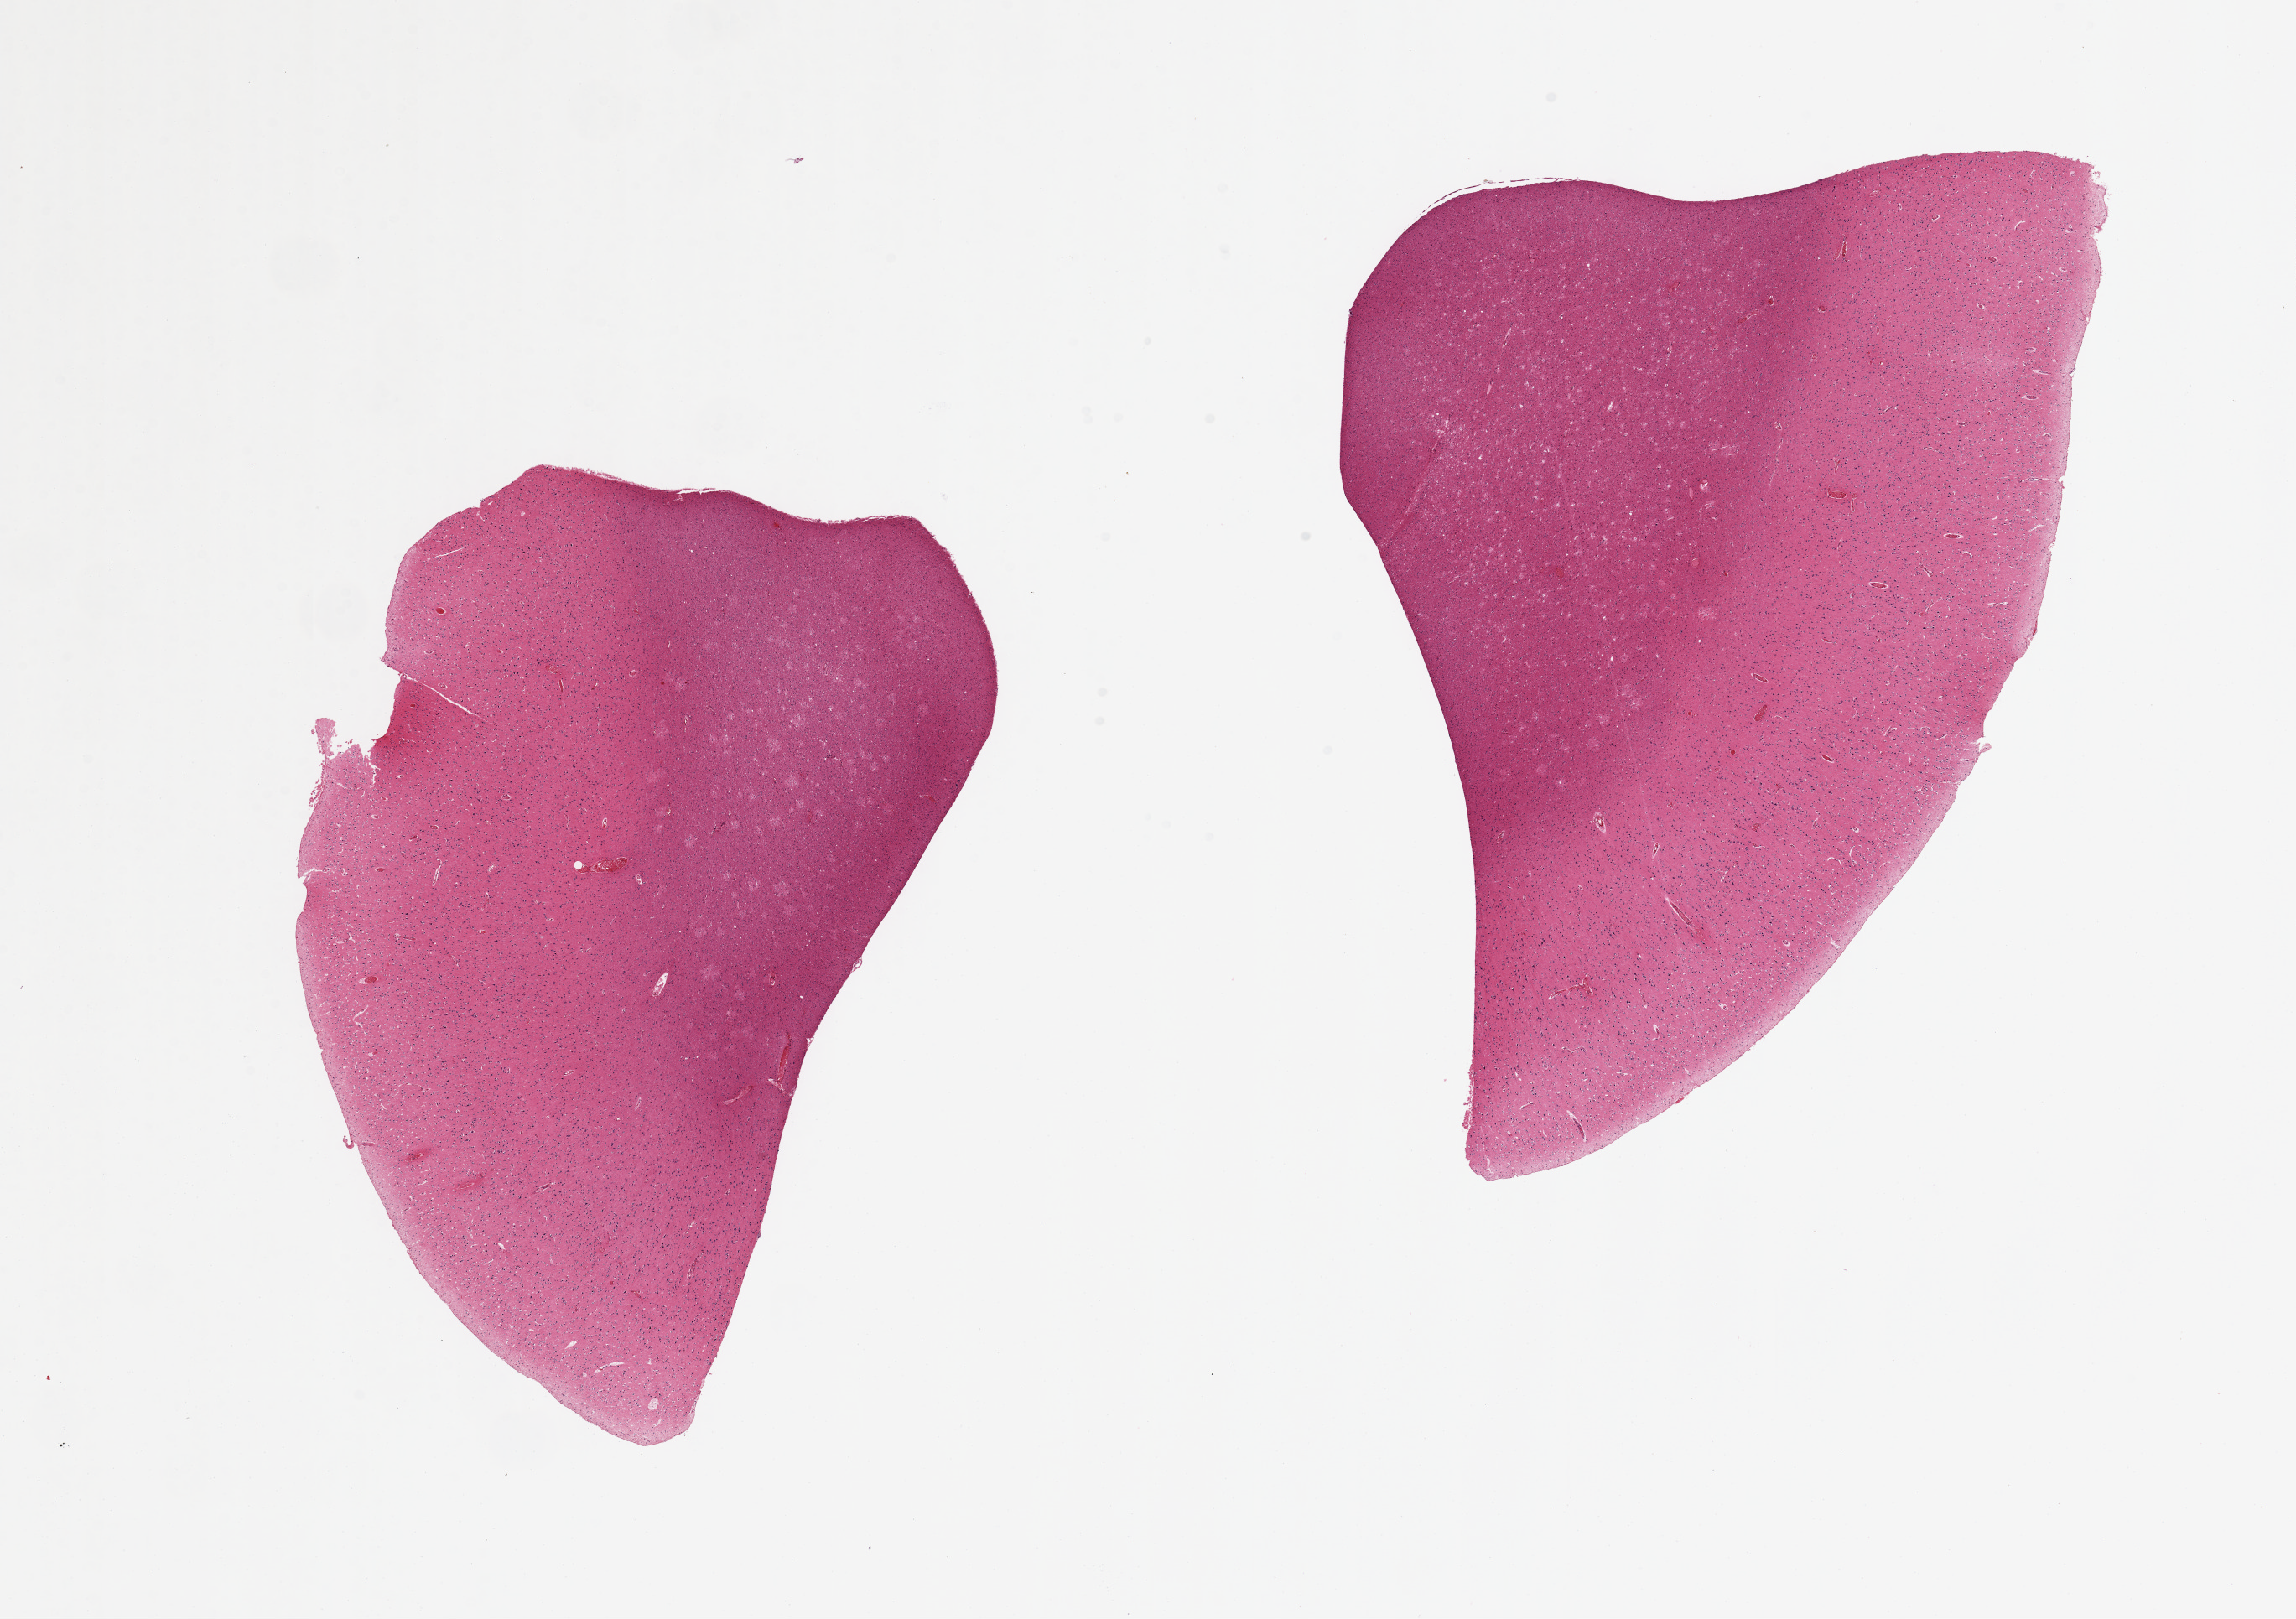
Digitized hematoxylin and eosin (H&E)-stained section, brightfield, whole scanned area (about 21.7 x 15.3 mm, from a 20x scan) shown as a low-resolution overview; PAXgene-fixed paraffin-embedded (PFPE) section; section of cerebral cortex (target tissue); donor tissue sample. Male donor.
* pathologist's review note for this sample: 2 pieces